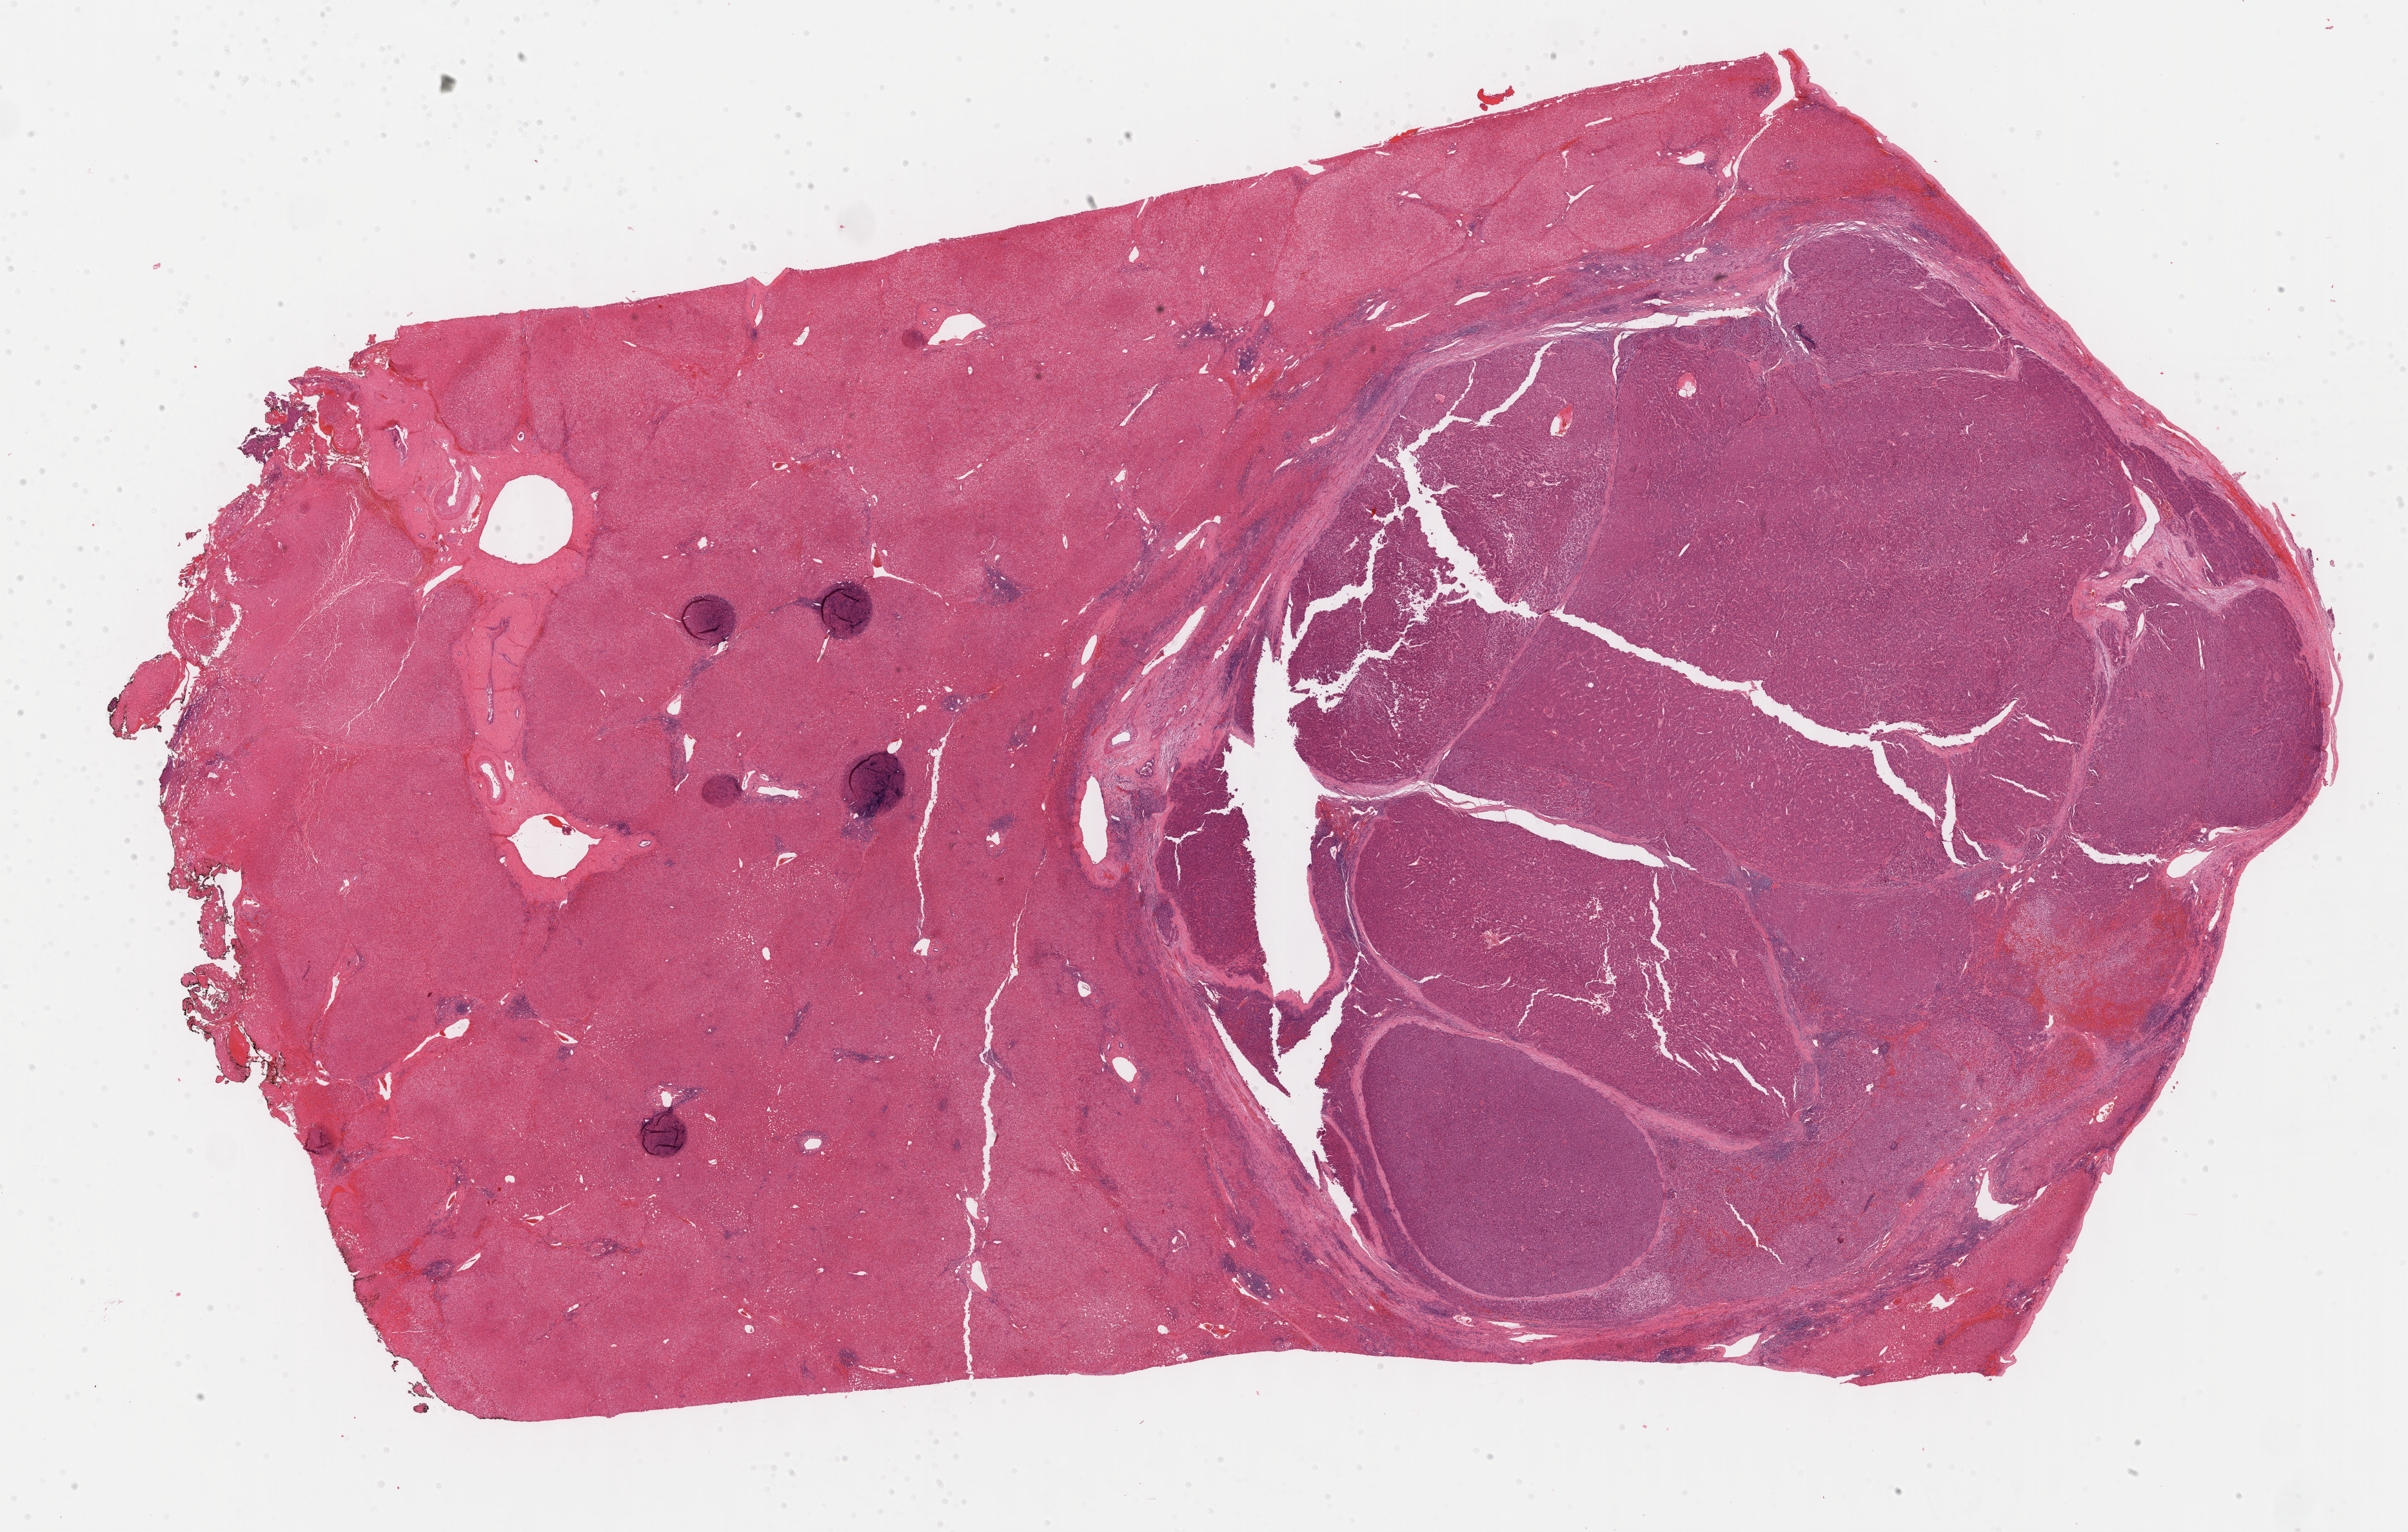
Whole-slide histology image, Hematoxylin and eosin (H&E) stained — low-resolution overview of the scanned area, about 30.2 x 19.2 mm; formalin-fixed paraffin-embedded (FFPE) diagnostic section; liver, primary tumour sample. Male patient; age at initial diagnosis 72 years. Histologic grade: G1 (well differentiated).
Diagnosis: Hepatocellular carcinoma, NOS.